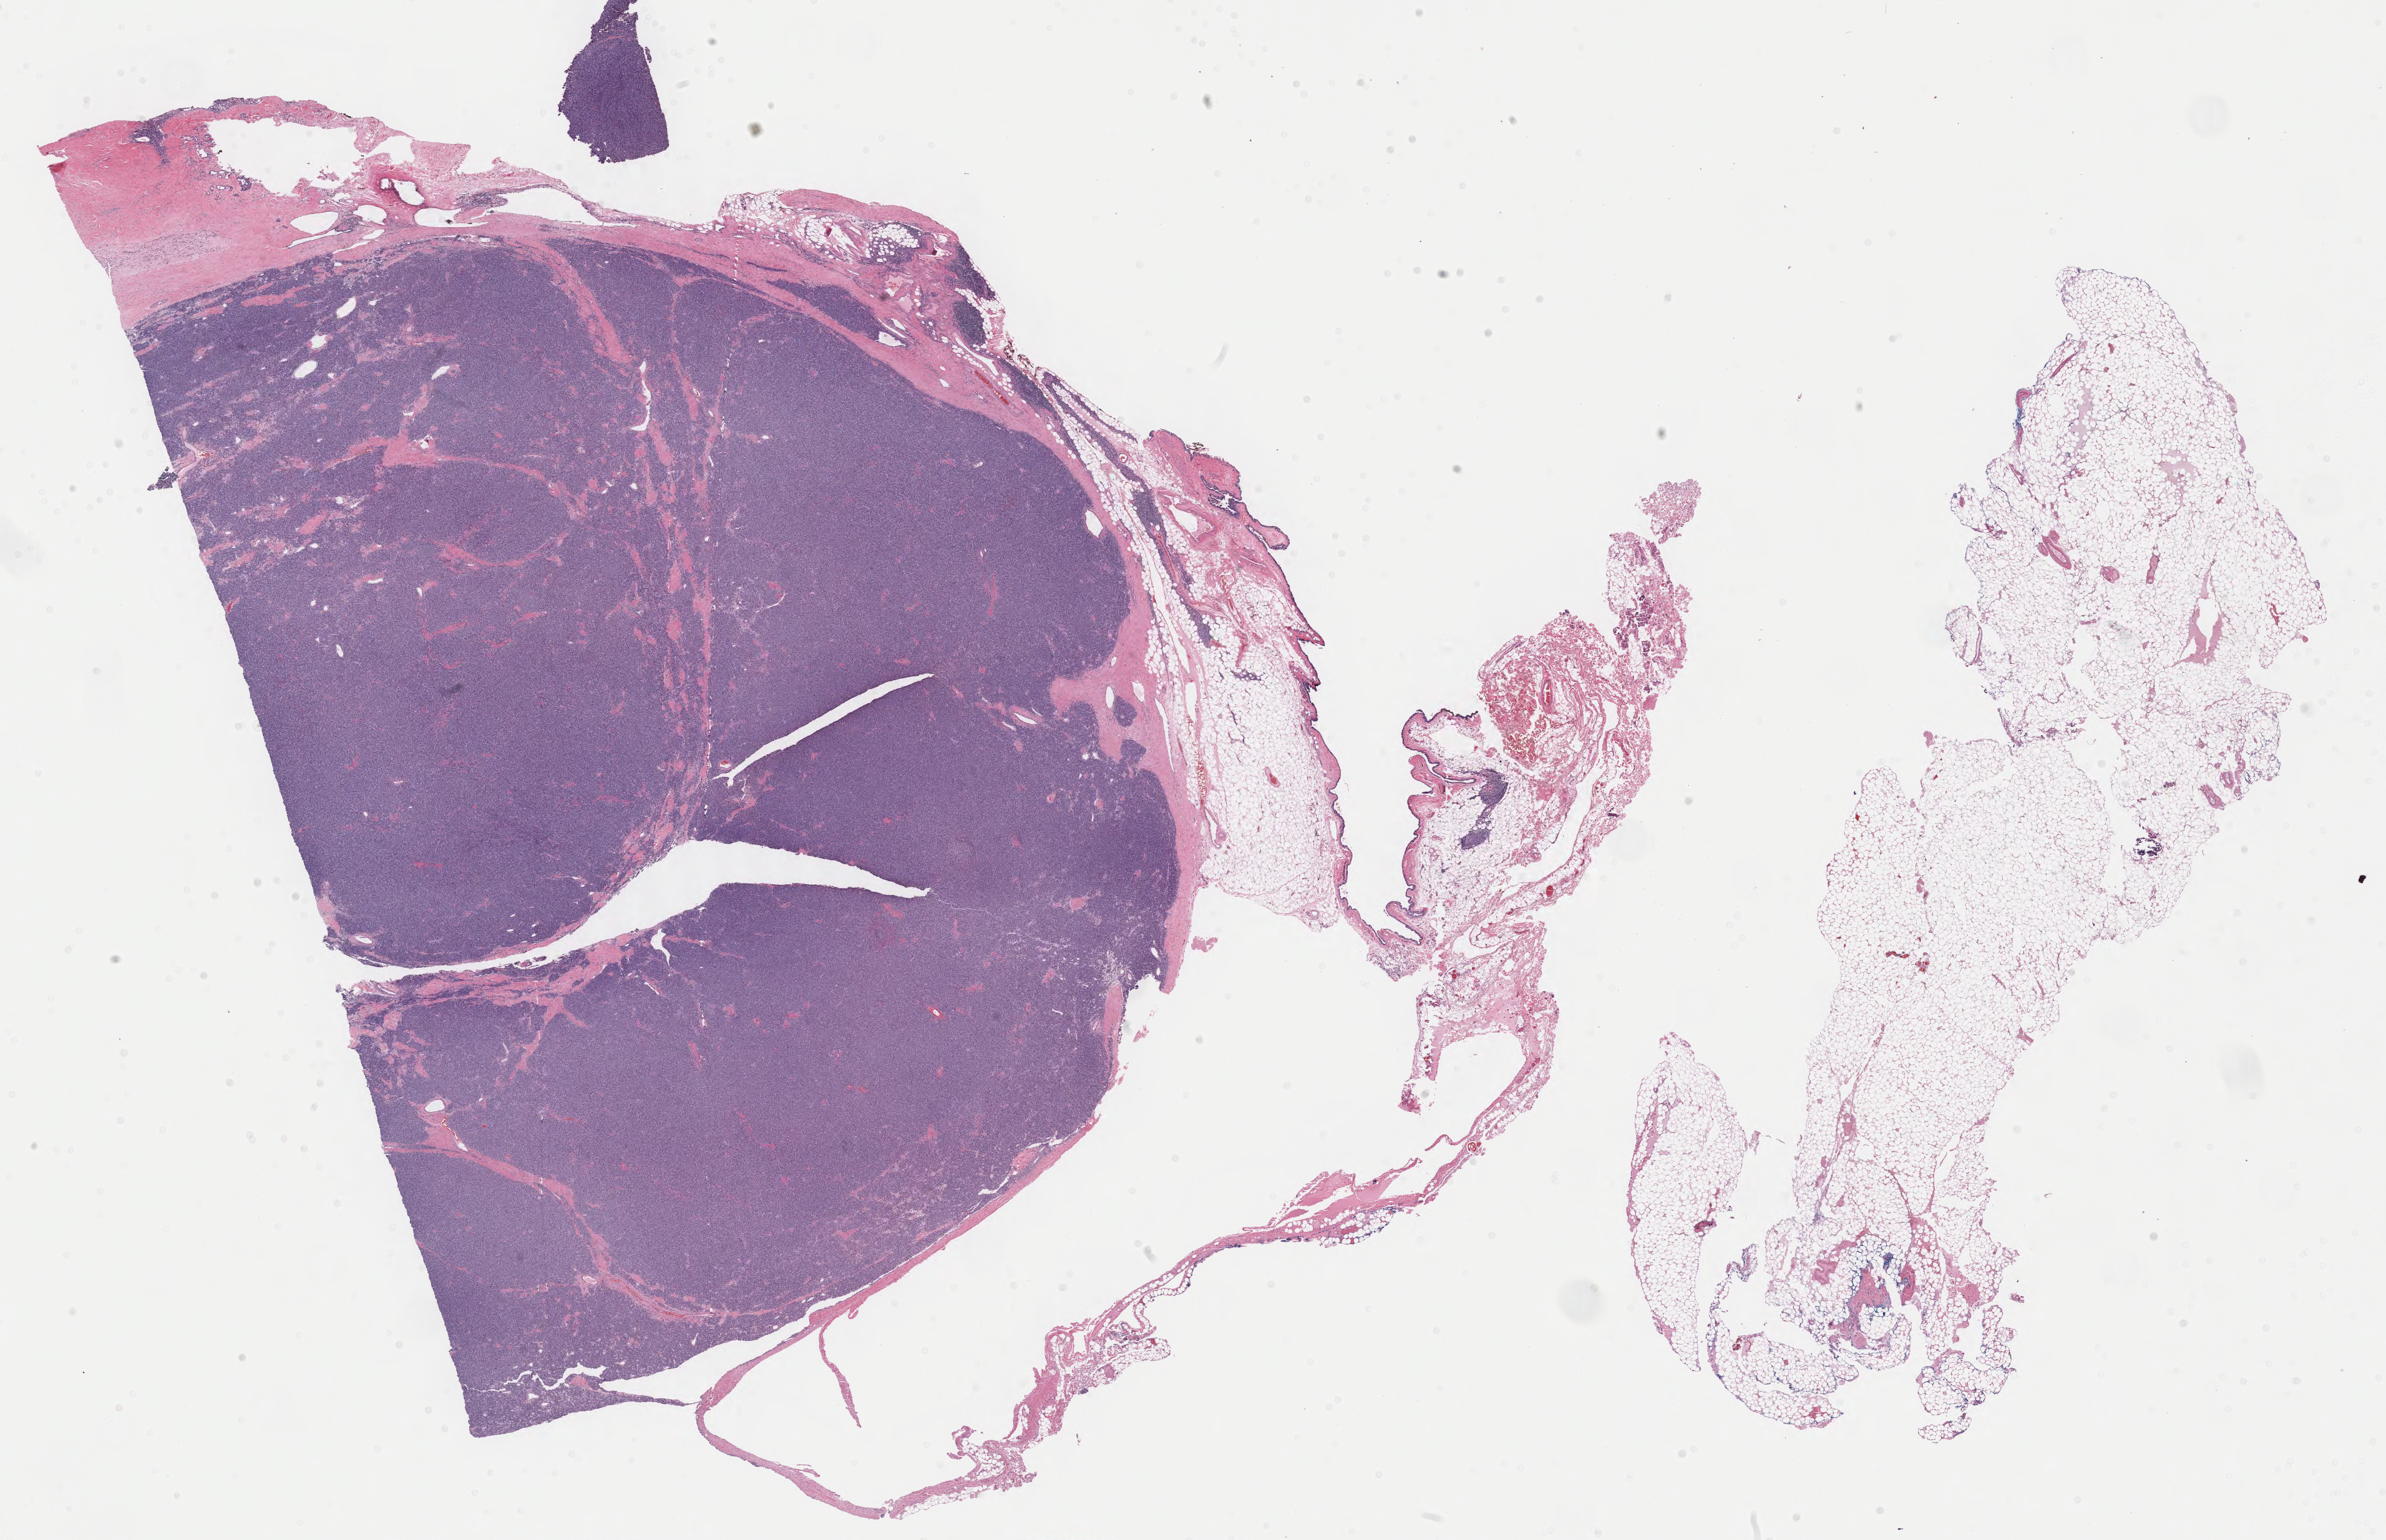
H&E-stained whole-slide image, low-resolution overview of the scanned area, about 30.3 x 19.6 mm; formalin-fixed paraffin-embedded (FFPE) diagnostic section; sample: primary tumour, thymus. Patient: male, age at initial diagnosis 52 years.
Pathologic diagnosis: Thymoma, type A, malignant.